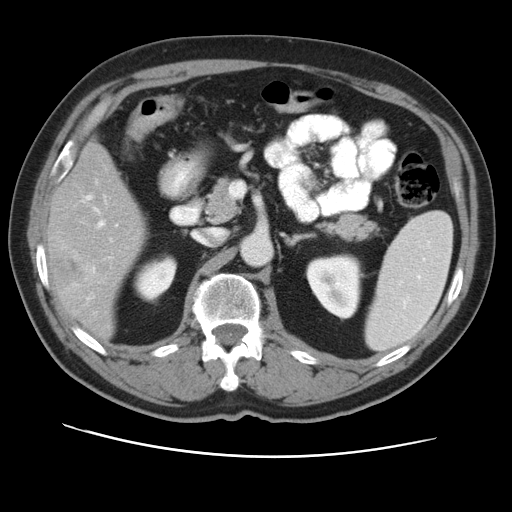
Contrast-enhanced abdominal CT, one axial slice; position 23 of 49 along the scan axis; reconstruction kernel STANDARD; intravenous contrast given; soft-tissue window (W 400 / L 40 HU); 512 × 512 image matrix, field of view 374 × 374 mm. Male patient, age 59 years. Case-level facts recorded for this patient, not image findings: diagnosis: colorectal cancer liver metastases, imaged before liver resection; multiple liver metastases: yes; largest metastasis: 6.3 cm; disease in both lobes: yes.
Structures marked on this image (expert manual segmentation):
- hepatic veins: box from (x=87, y=195) to (x=91, y=199) px
- liver: (x=48, y=144)–(x=143, y=337)
- planned liver remnant (the part of the liver to remain after resection): (x=52, y=144)–(x=143, y=337)
- portal vein (with intrahepatic branches): (x=92, y=221)–(x=105, y=272)
- liver metastasis: (x=55, y=250)–(x=85, y=287)